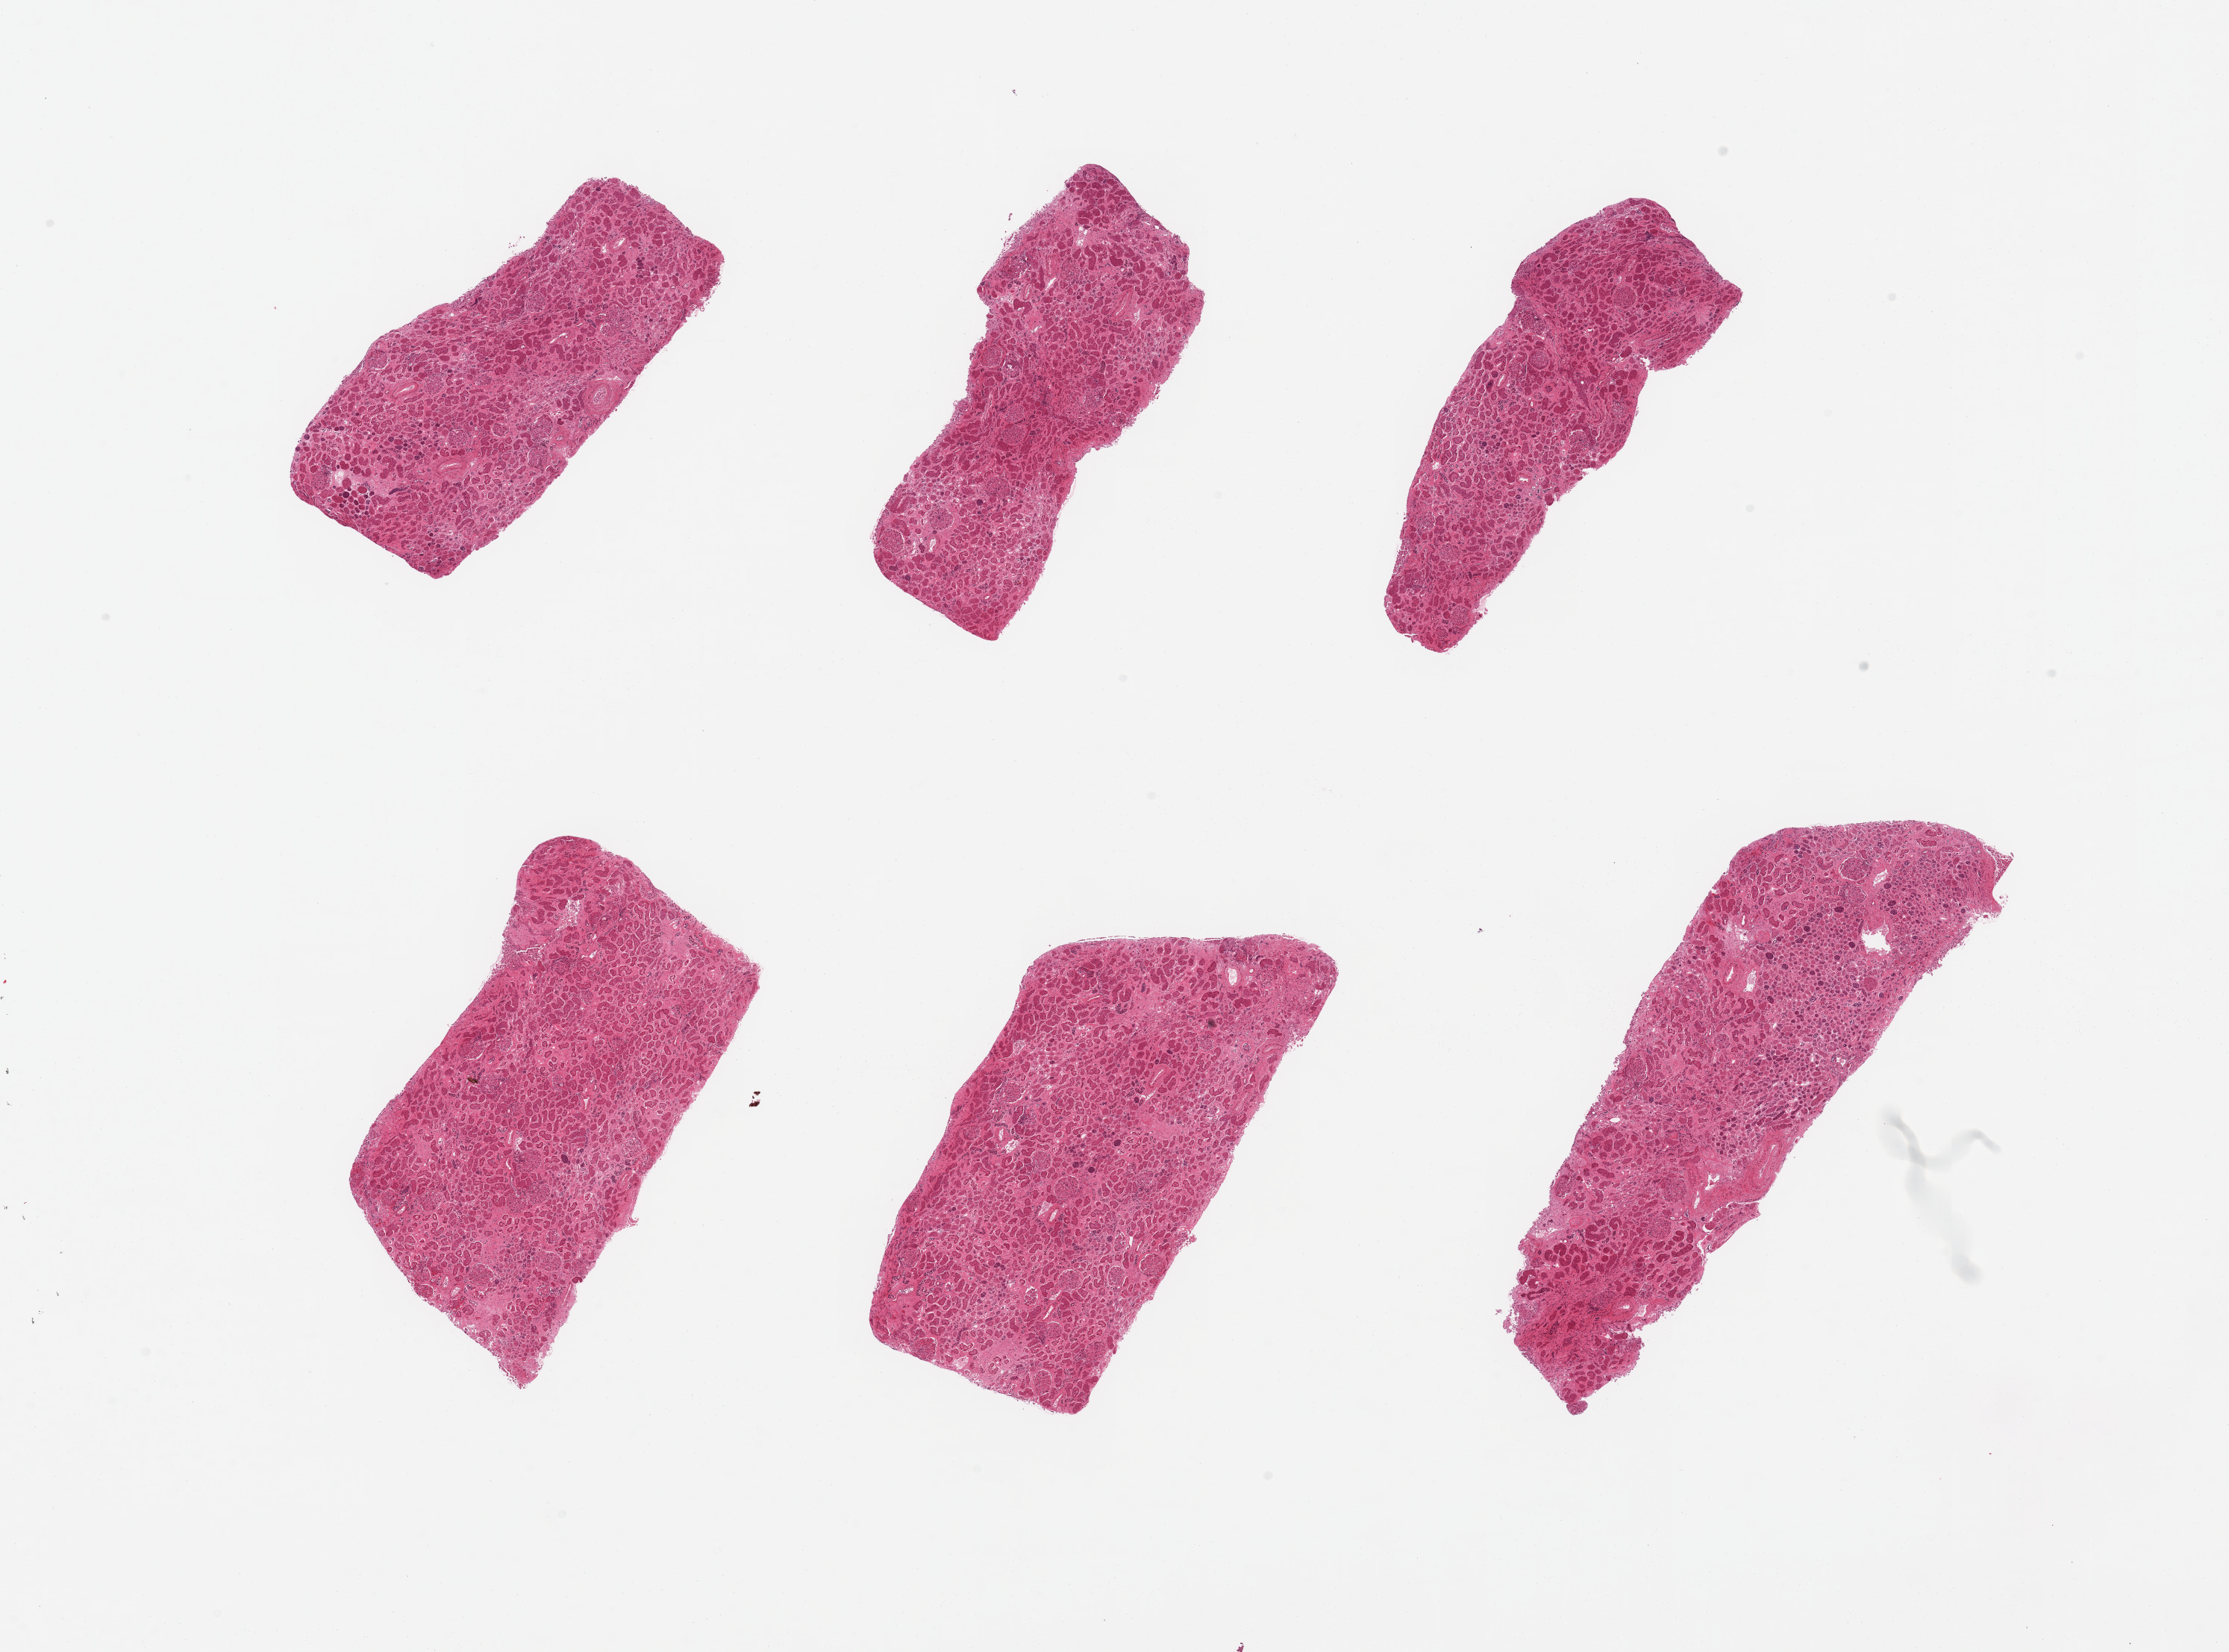
Haematoxylin and eosin whole-slide image, brightfield, a low-resolution overview of the entire scanned area, about 23.6 x 17.5 mm (acquisition: 20x scan); PAXgene-fixed paraffin-embedded (PFPE) section; section of renal cortex (target tissue); donor tissue sample. Male donor.
* reviewer comment on this tissue sample: 6 pieces, advanced tubular autolysis; glomeruli present